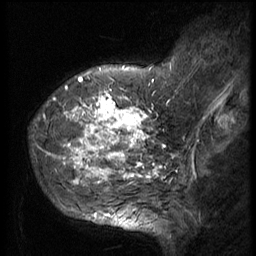
Breast MRI (dynamic contrast-enhanced), one sagittal slice; position 14 of 56 along the scan axis; 3 images stored at this slice position (order not interpretable as contrast timing); 1.5 T; TE 4.2 ms, TR 9 ms; 2.5 mm slice thickness; 256 × 256 image matrix, field of view 180 × 180 mm. Patient: female, 49 years. Case-level facts recorded for this patient, not image findings: setting: breast cancer imaged before/during neoadjuvant chemotherapy; receptor status: HER2-positive.
Annotated regions visible in this slice (semi-automatically segmented with operator editing):
- analysis volume of interest (the breast-tissue region the enhancement analysis was run in; not a lesion): bounding box [x1, y1, x2, y2] px = [37, 85, 156, 207]
- tumour enhancement mask (voxels above the 140 % enhancement threshold inside the analysis volume of interest): [43, 86, 155, 186]